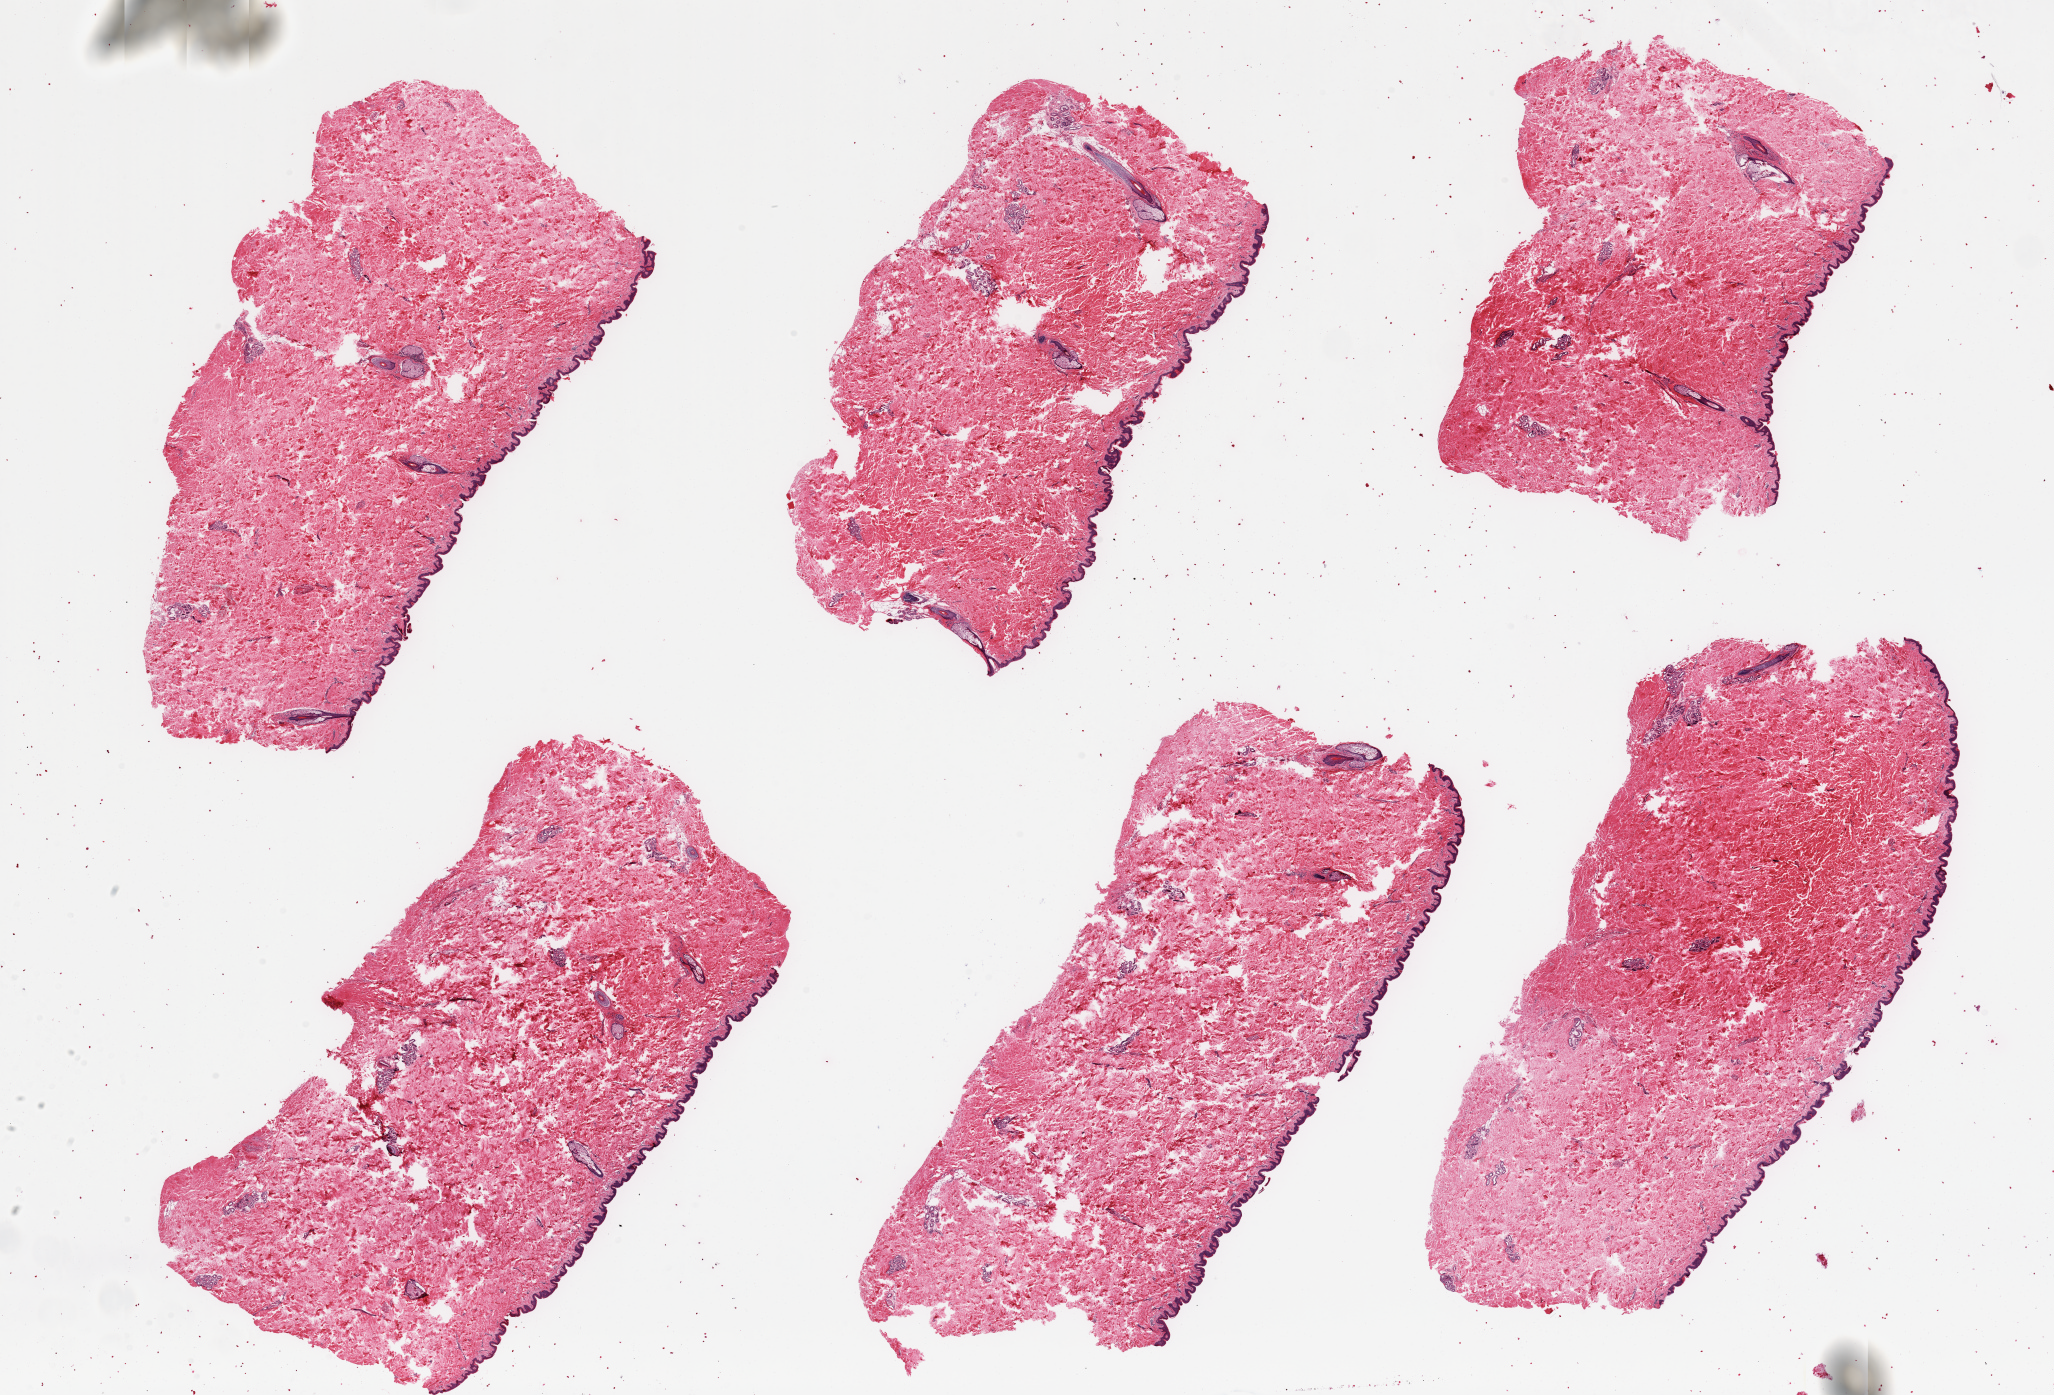
Hematoxylin and eosin (H&E) whole-slide image, a low-resolution overview of the entire scanned area, about 32.5 x 22.1 mm. PAXgene-fixed paraffin-embedded (PFPE) section. Sampled site (target tissue): skin of suprapubic region. Donor tissue sample. Donor sex: male.
Reviewer comment on this tissue sample: 6 pieces; well trimmed; <5% dermal fat.